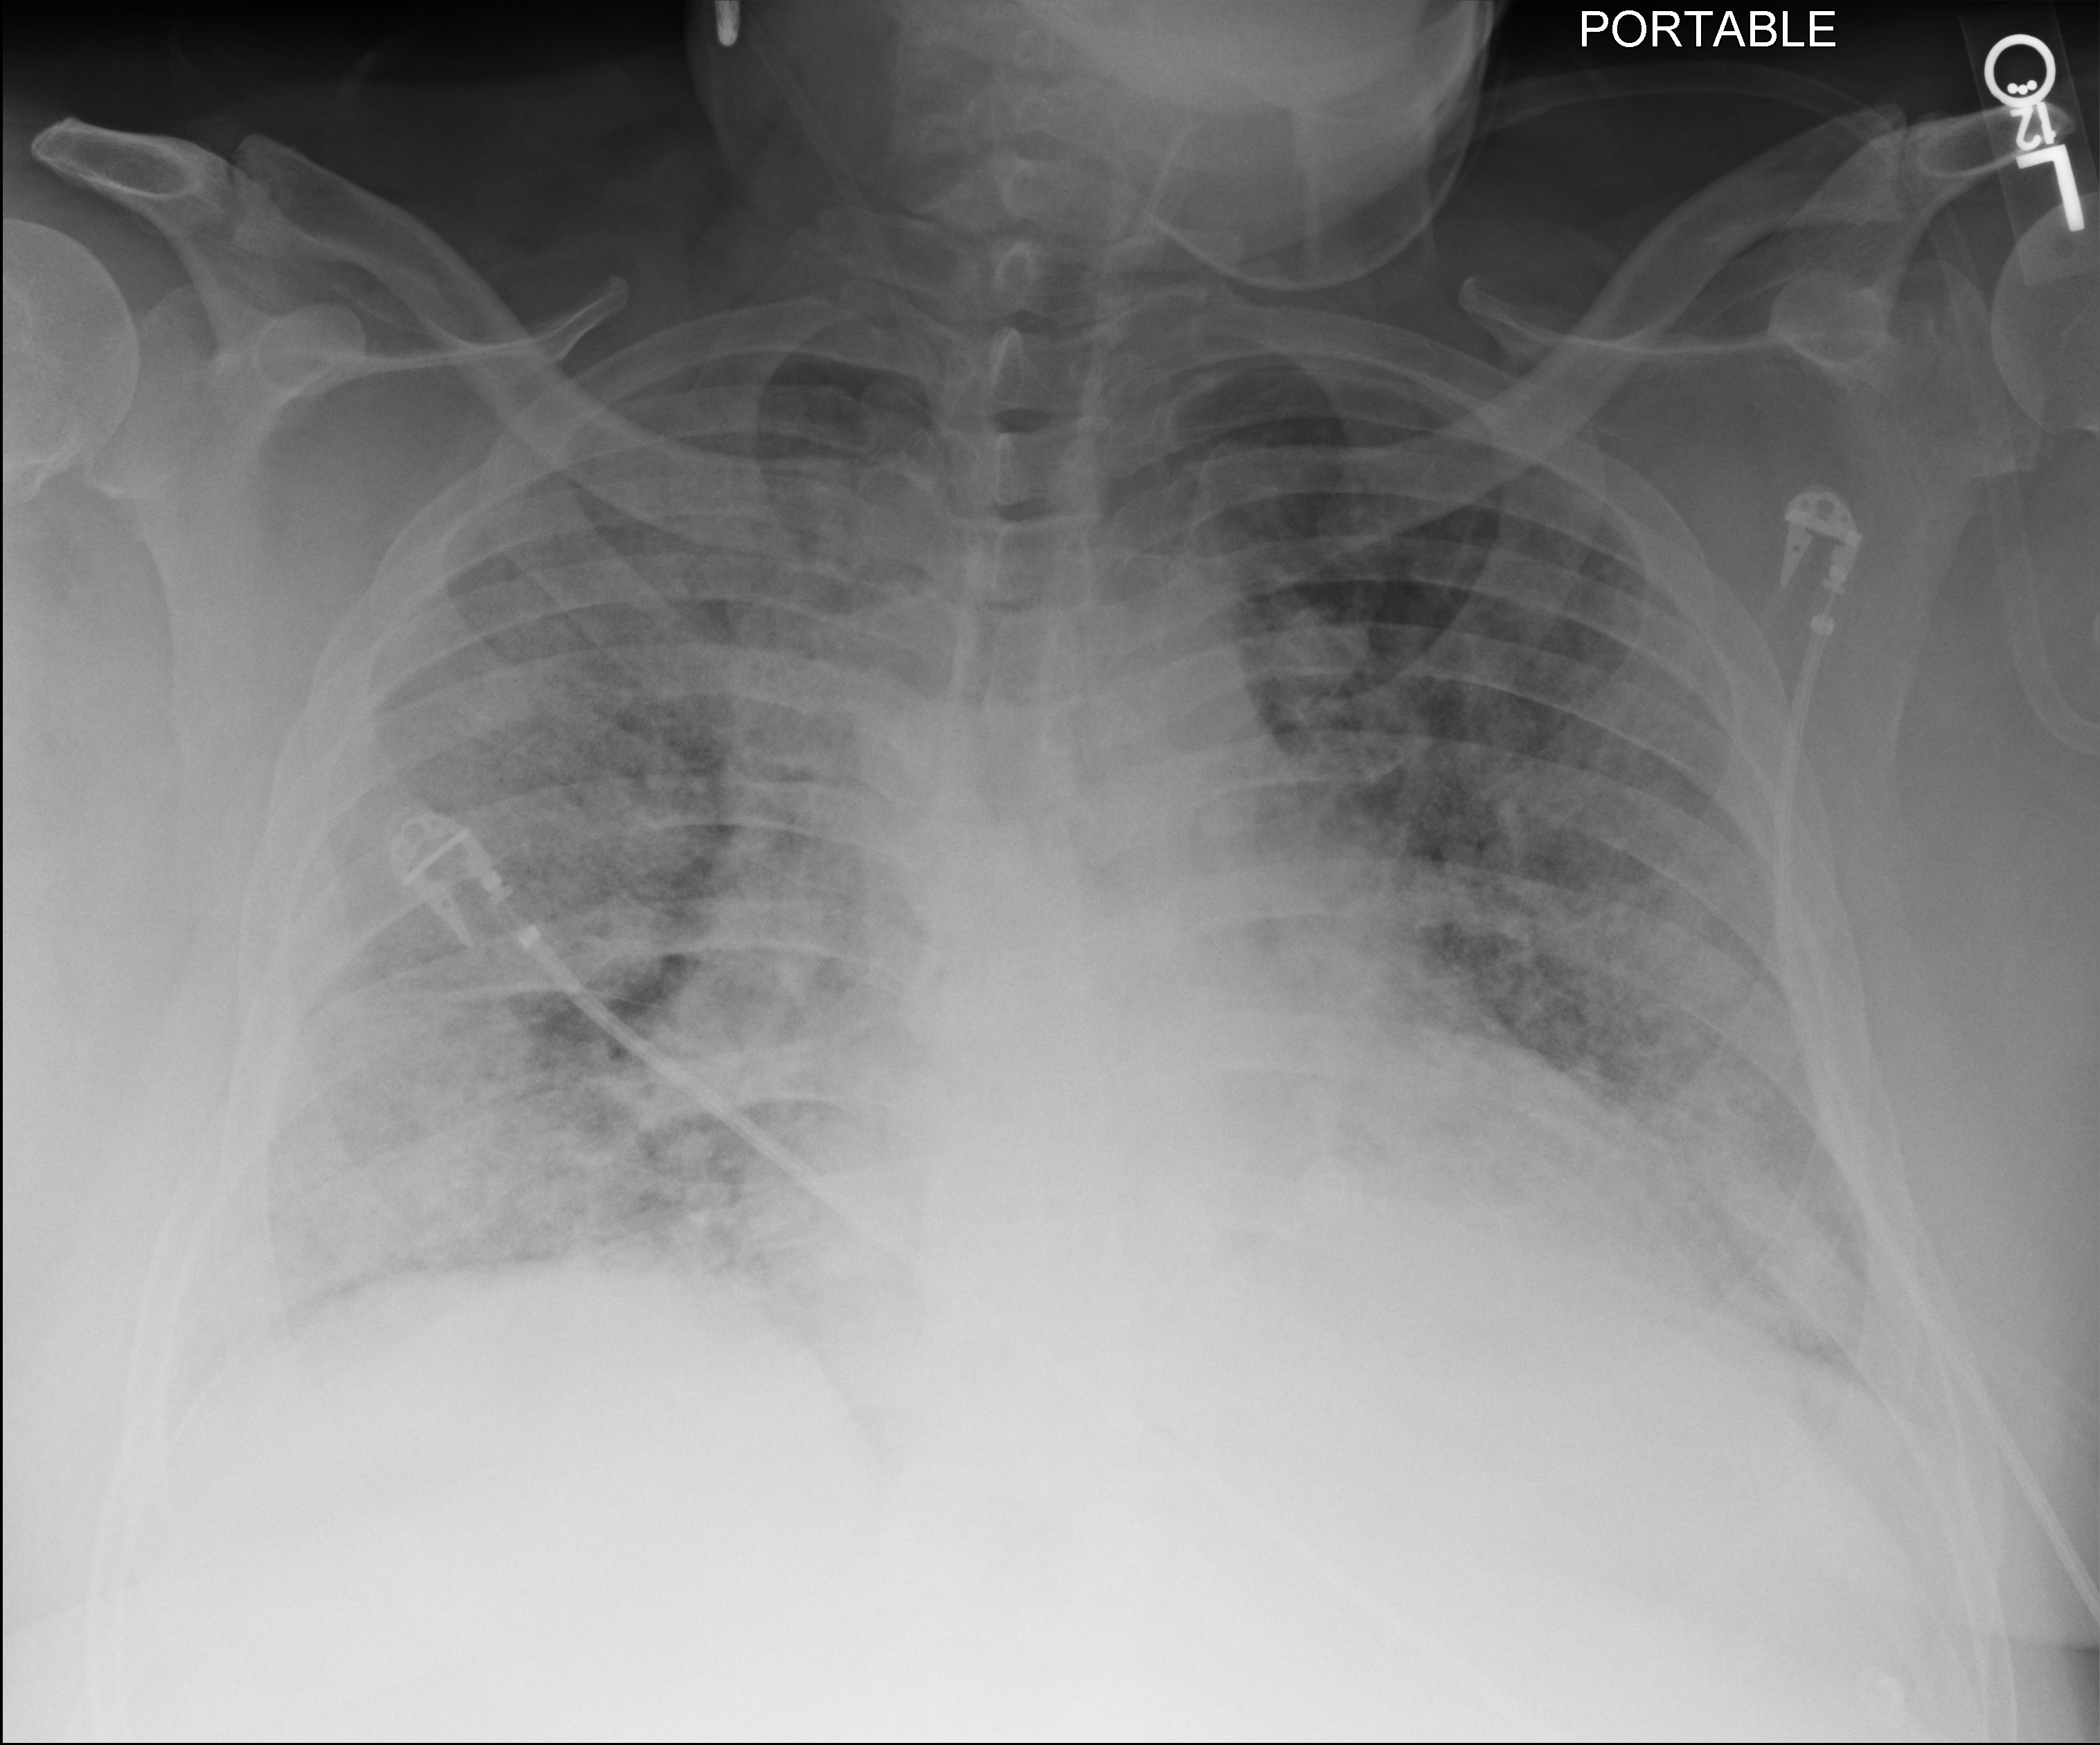
Bedside chest radiograph (computed radiography). Male patient hospitalised with COVID-19, age 60–74 years.
From the hospital-stay record, not from the radiograph (when in the stay this image was taken is not recorded):
- mechanically ventilated during this hospital stay: yes
- admitted to intensive care during this hospital stay: yes